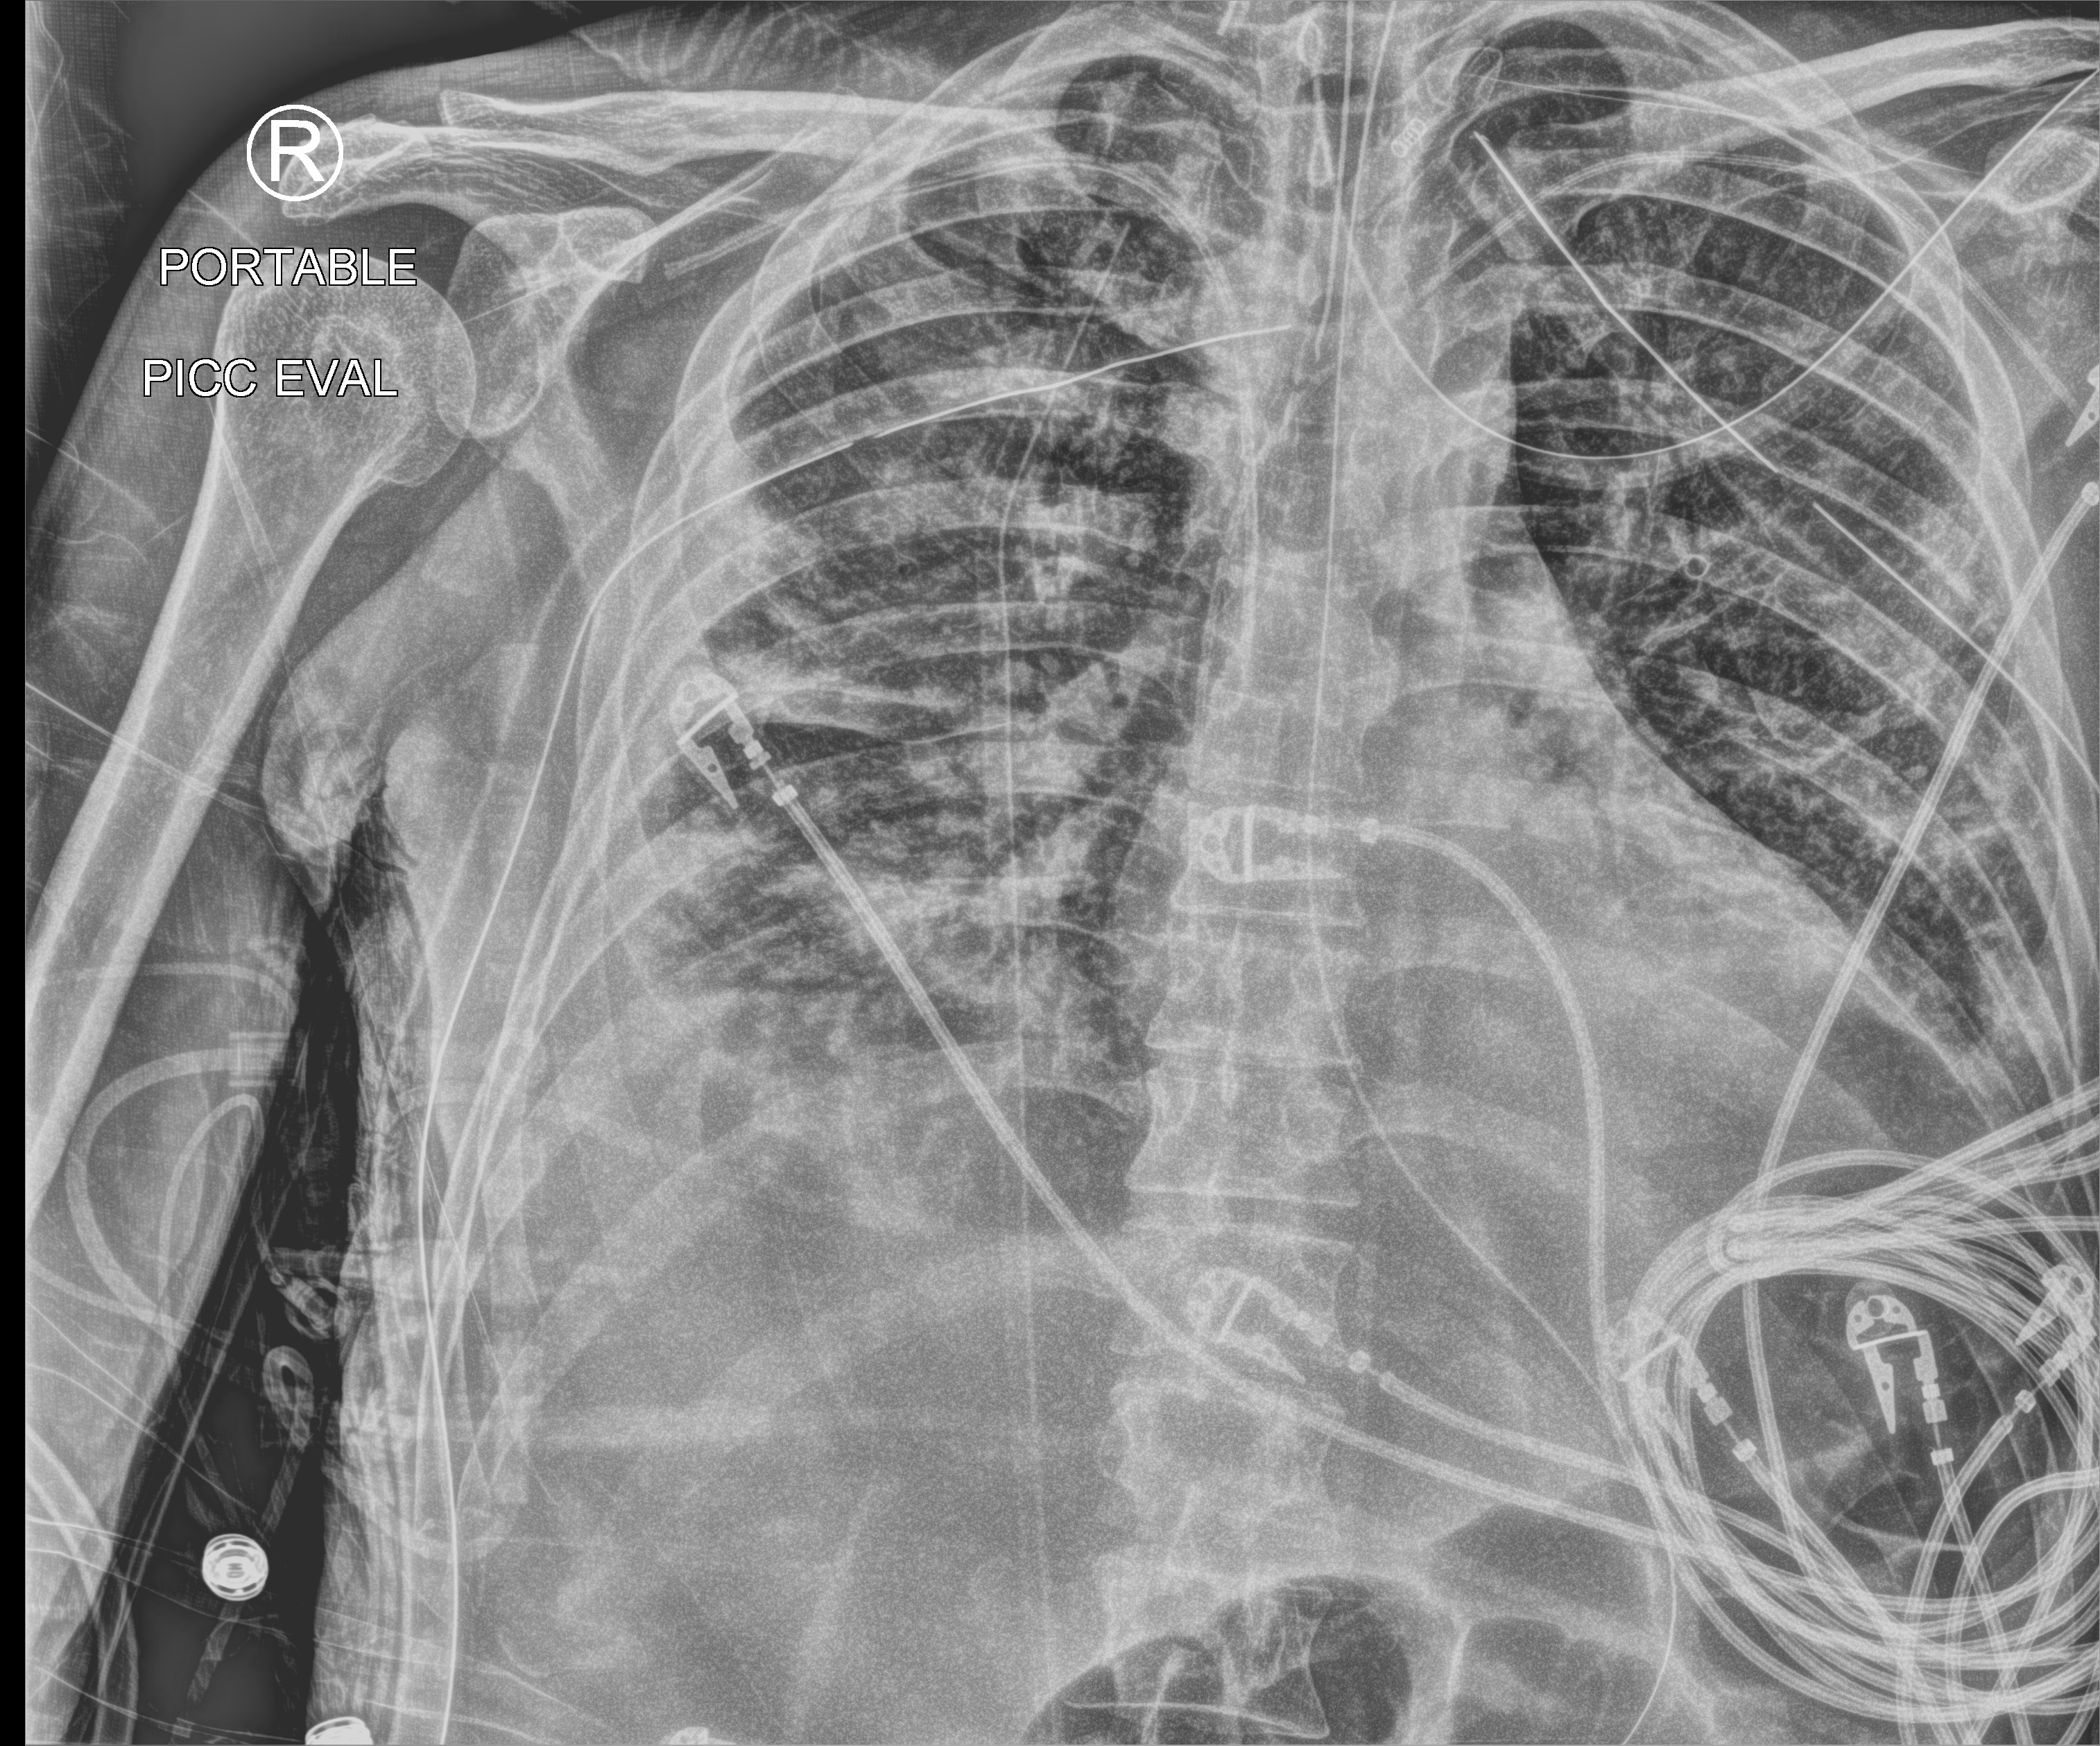
Bedside chest radiograph (computed radiography); anteroposterior (AP) projection. Male patient hospitalised with COVID-19, age 18–59 years.
Admission-level facts for this patient (not findings on this image; timing relative to this image not recorded): diabetes (admission record): yes; chronic kidney disease (admission record): no; admitted to intensive care during this hospital stay: yes.